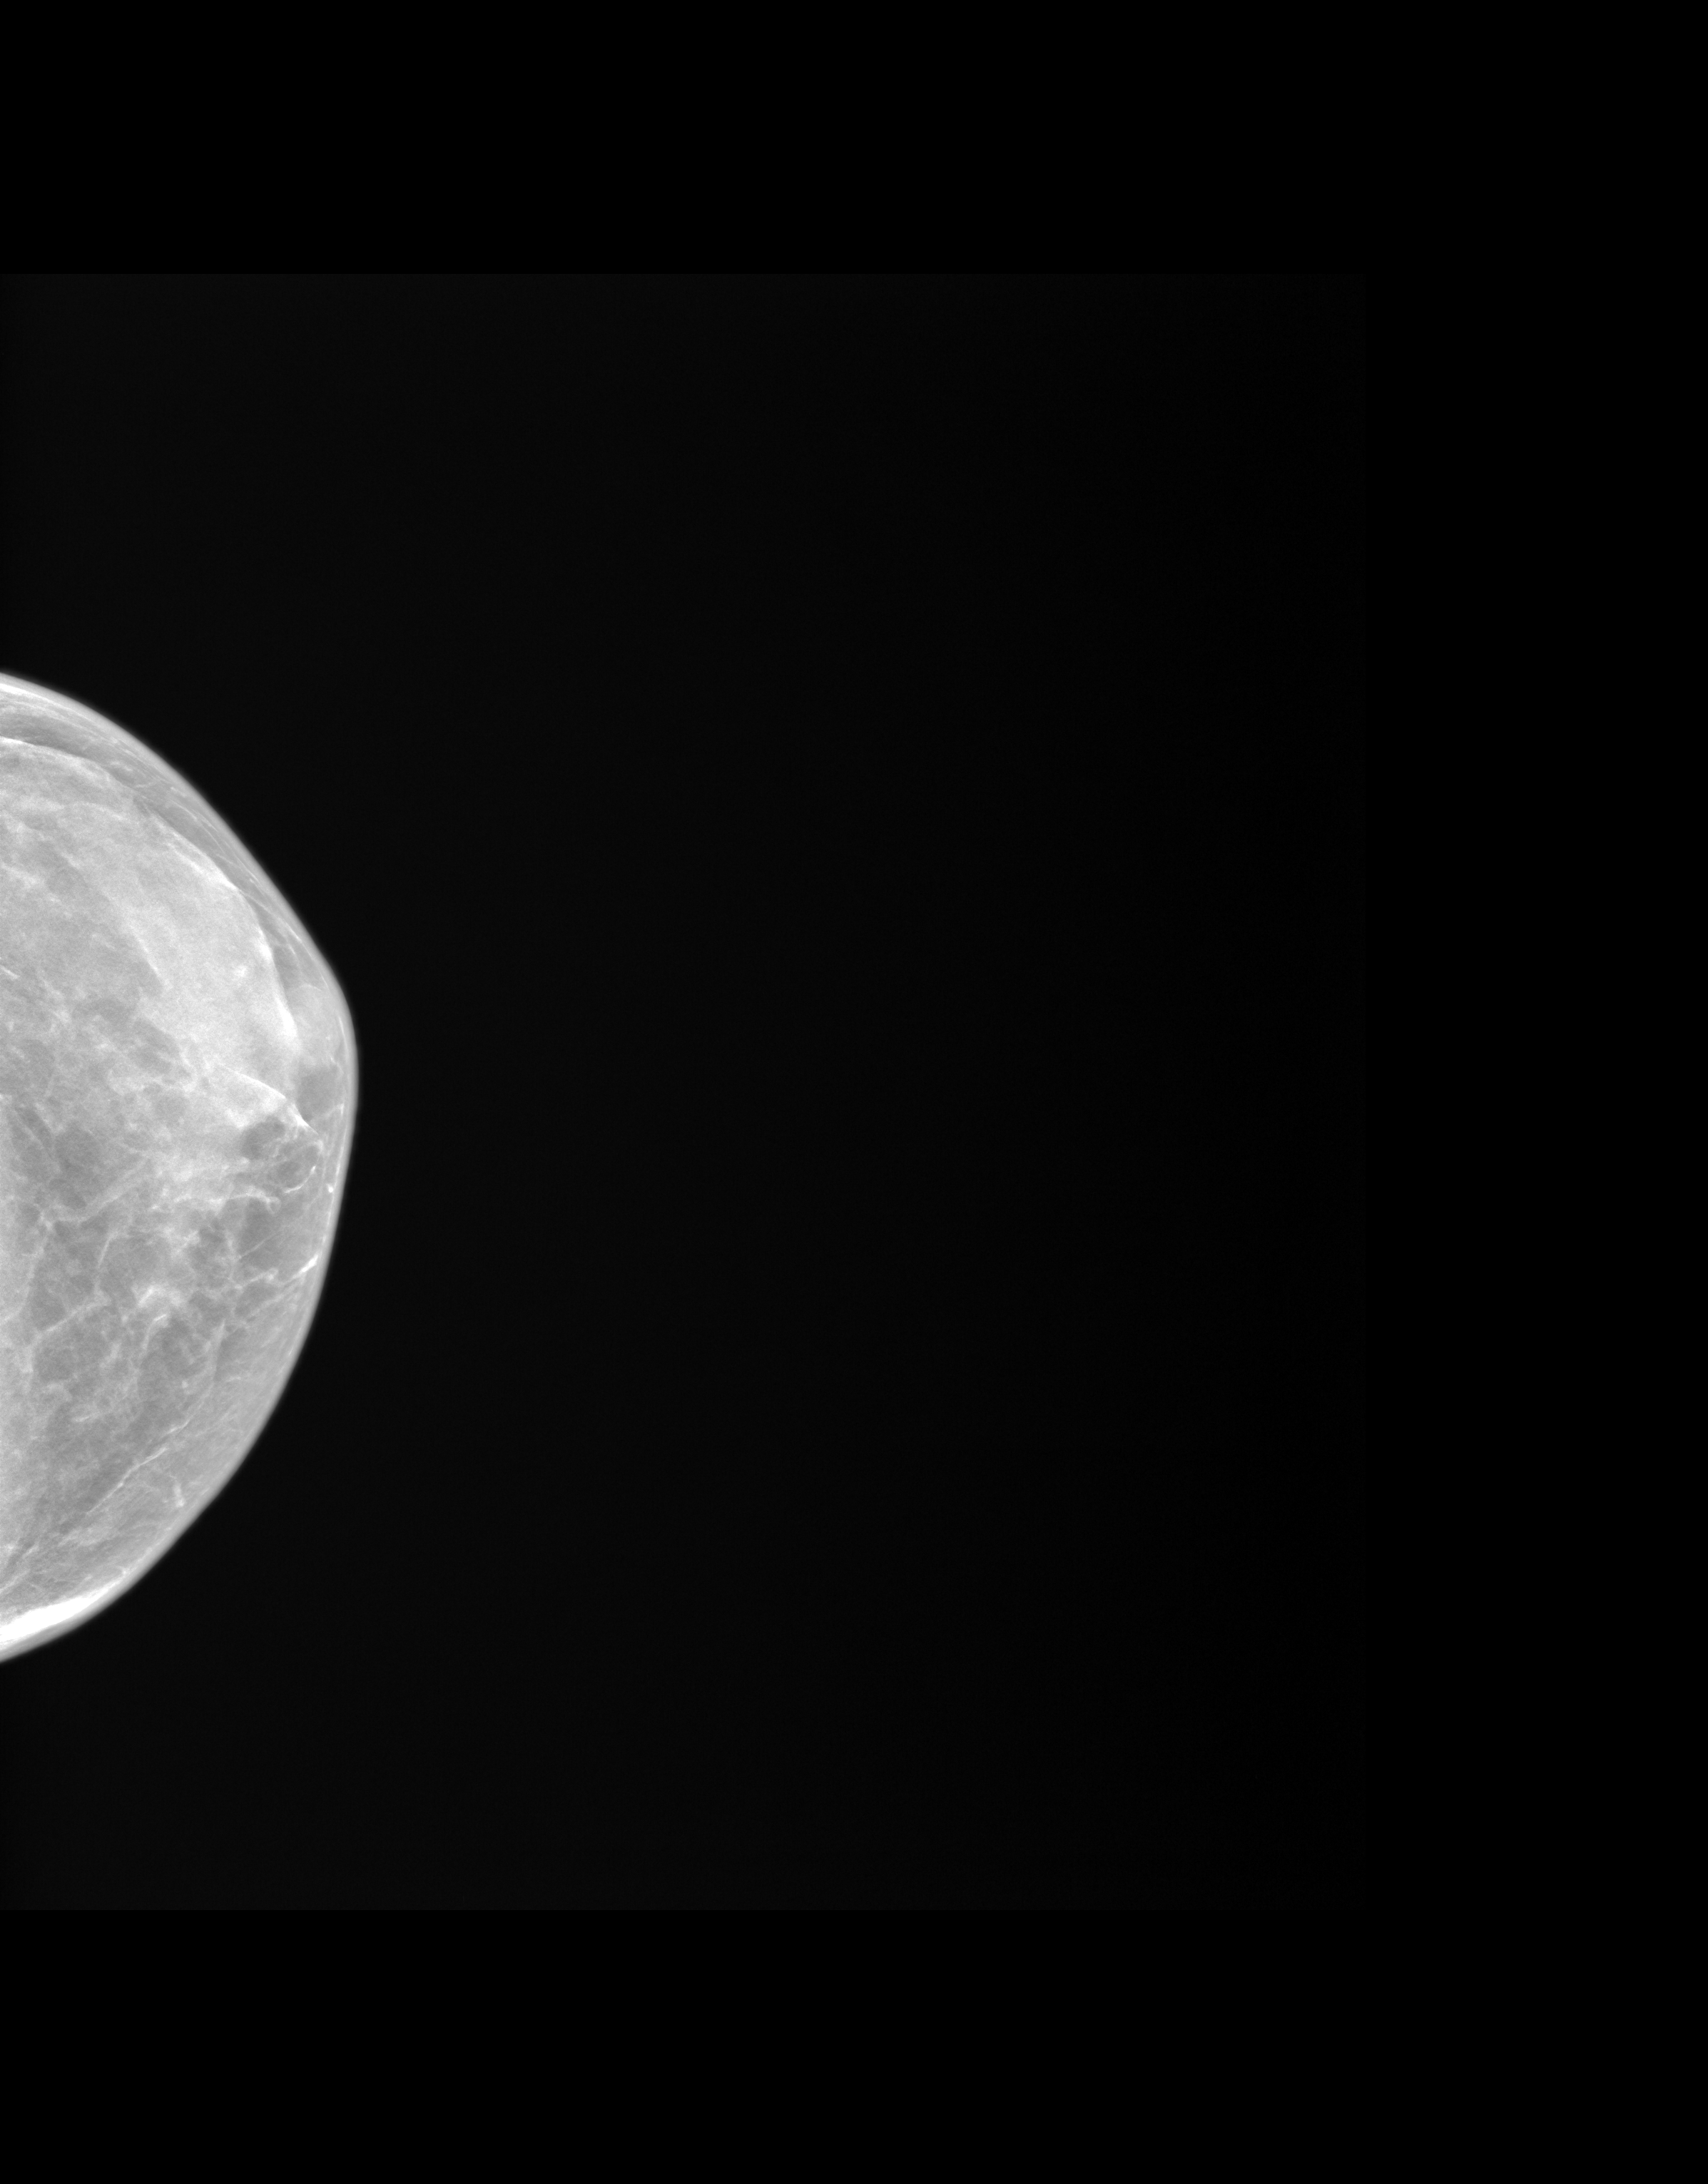
Screening examination. Female patient, age 56 years.
Image type: synthesized 2-D view from tomosynthesis. Breast: left. Projection: CC view.